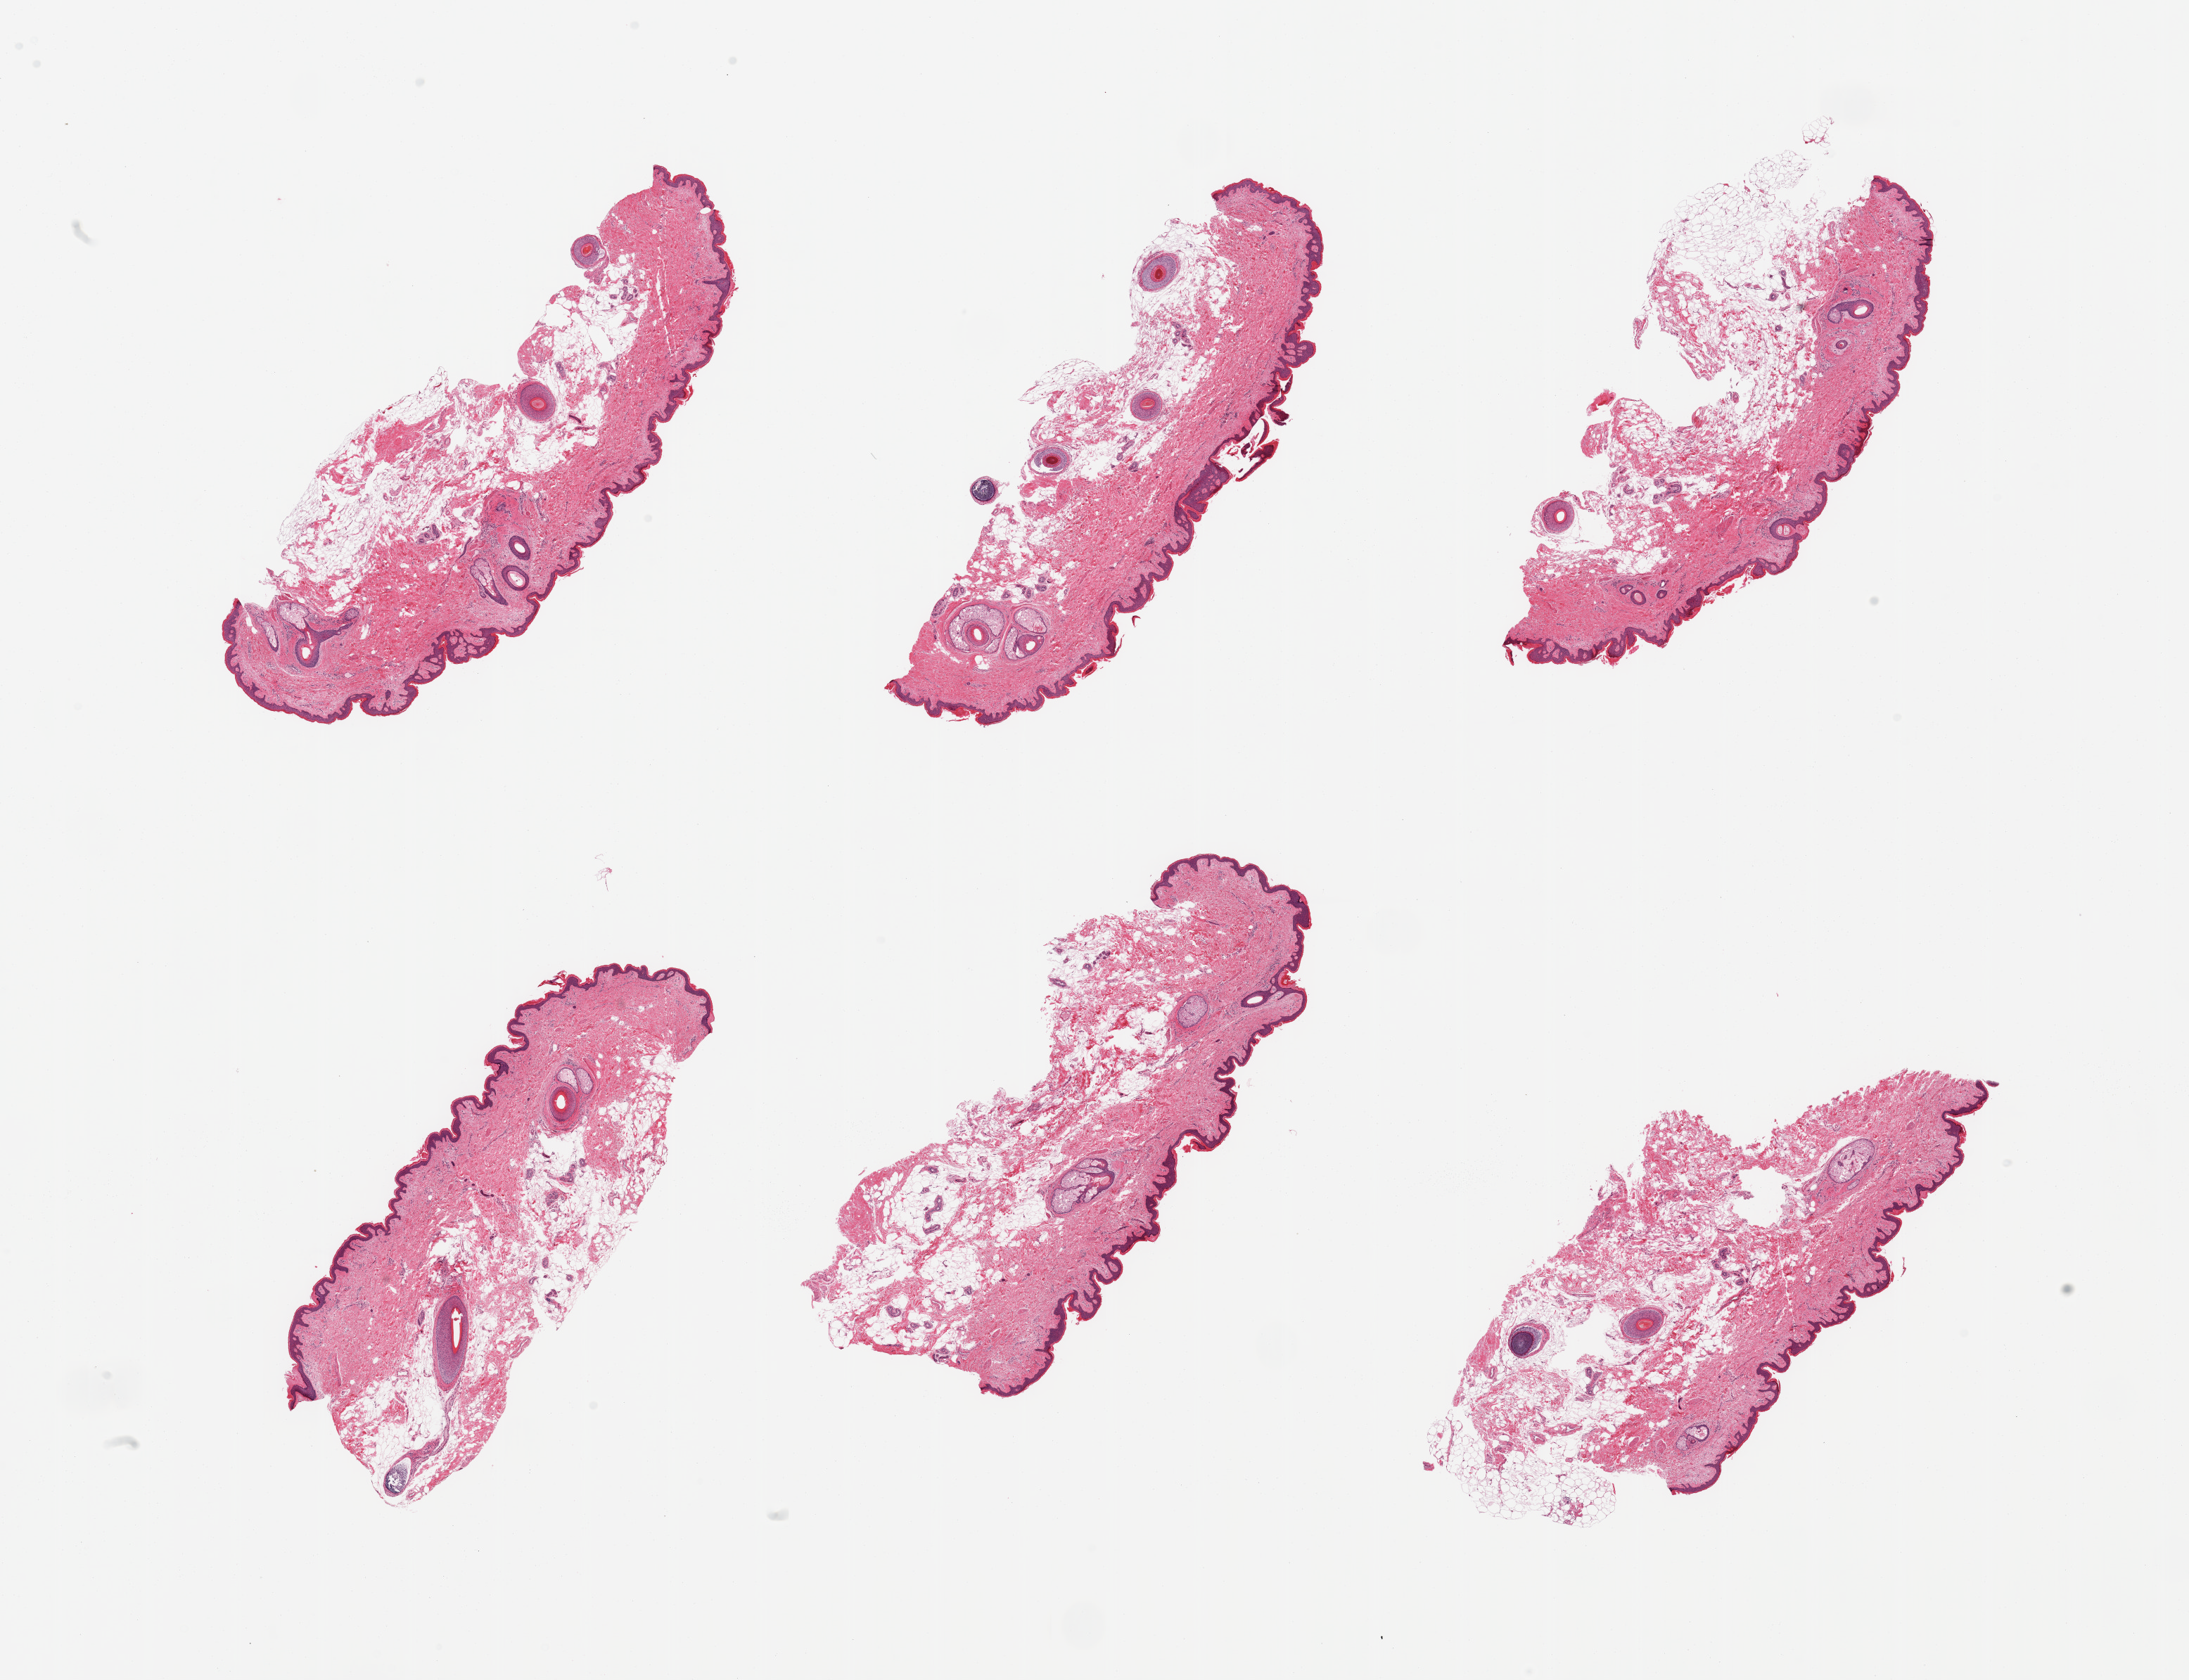
Hematoxylin and eosin (H&E) whole-slide image — low-resolution overview of the scanned area, about 24.6 x 18.9 mm (slide scanned at 20x), PAXgene-fixed, paraffin-embedded tissue, sampled site (target tissue): skin of suprapubic region, tissue donor sample. Male donor.
Reviewer comment on this tissue sample: 6 pieces, moderately abundant dermal fat up to ~2mm; Squamous epithelium is ~30-40 microns.